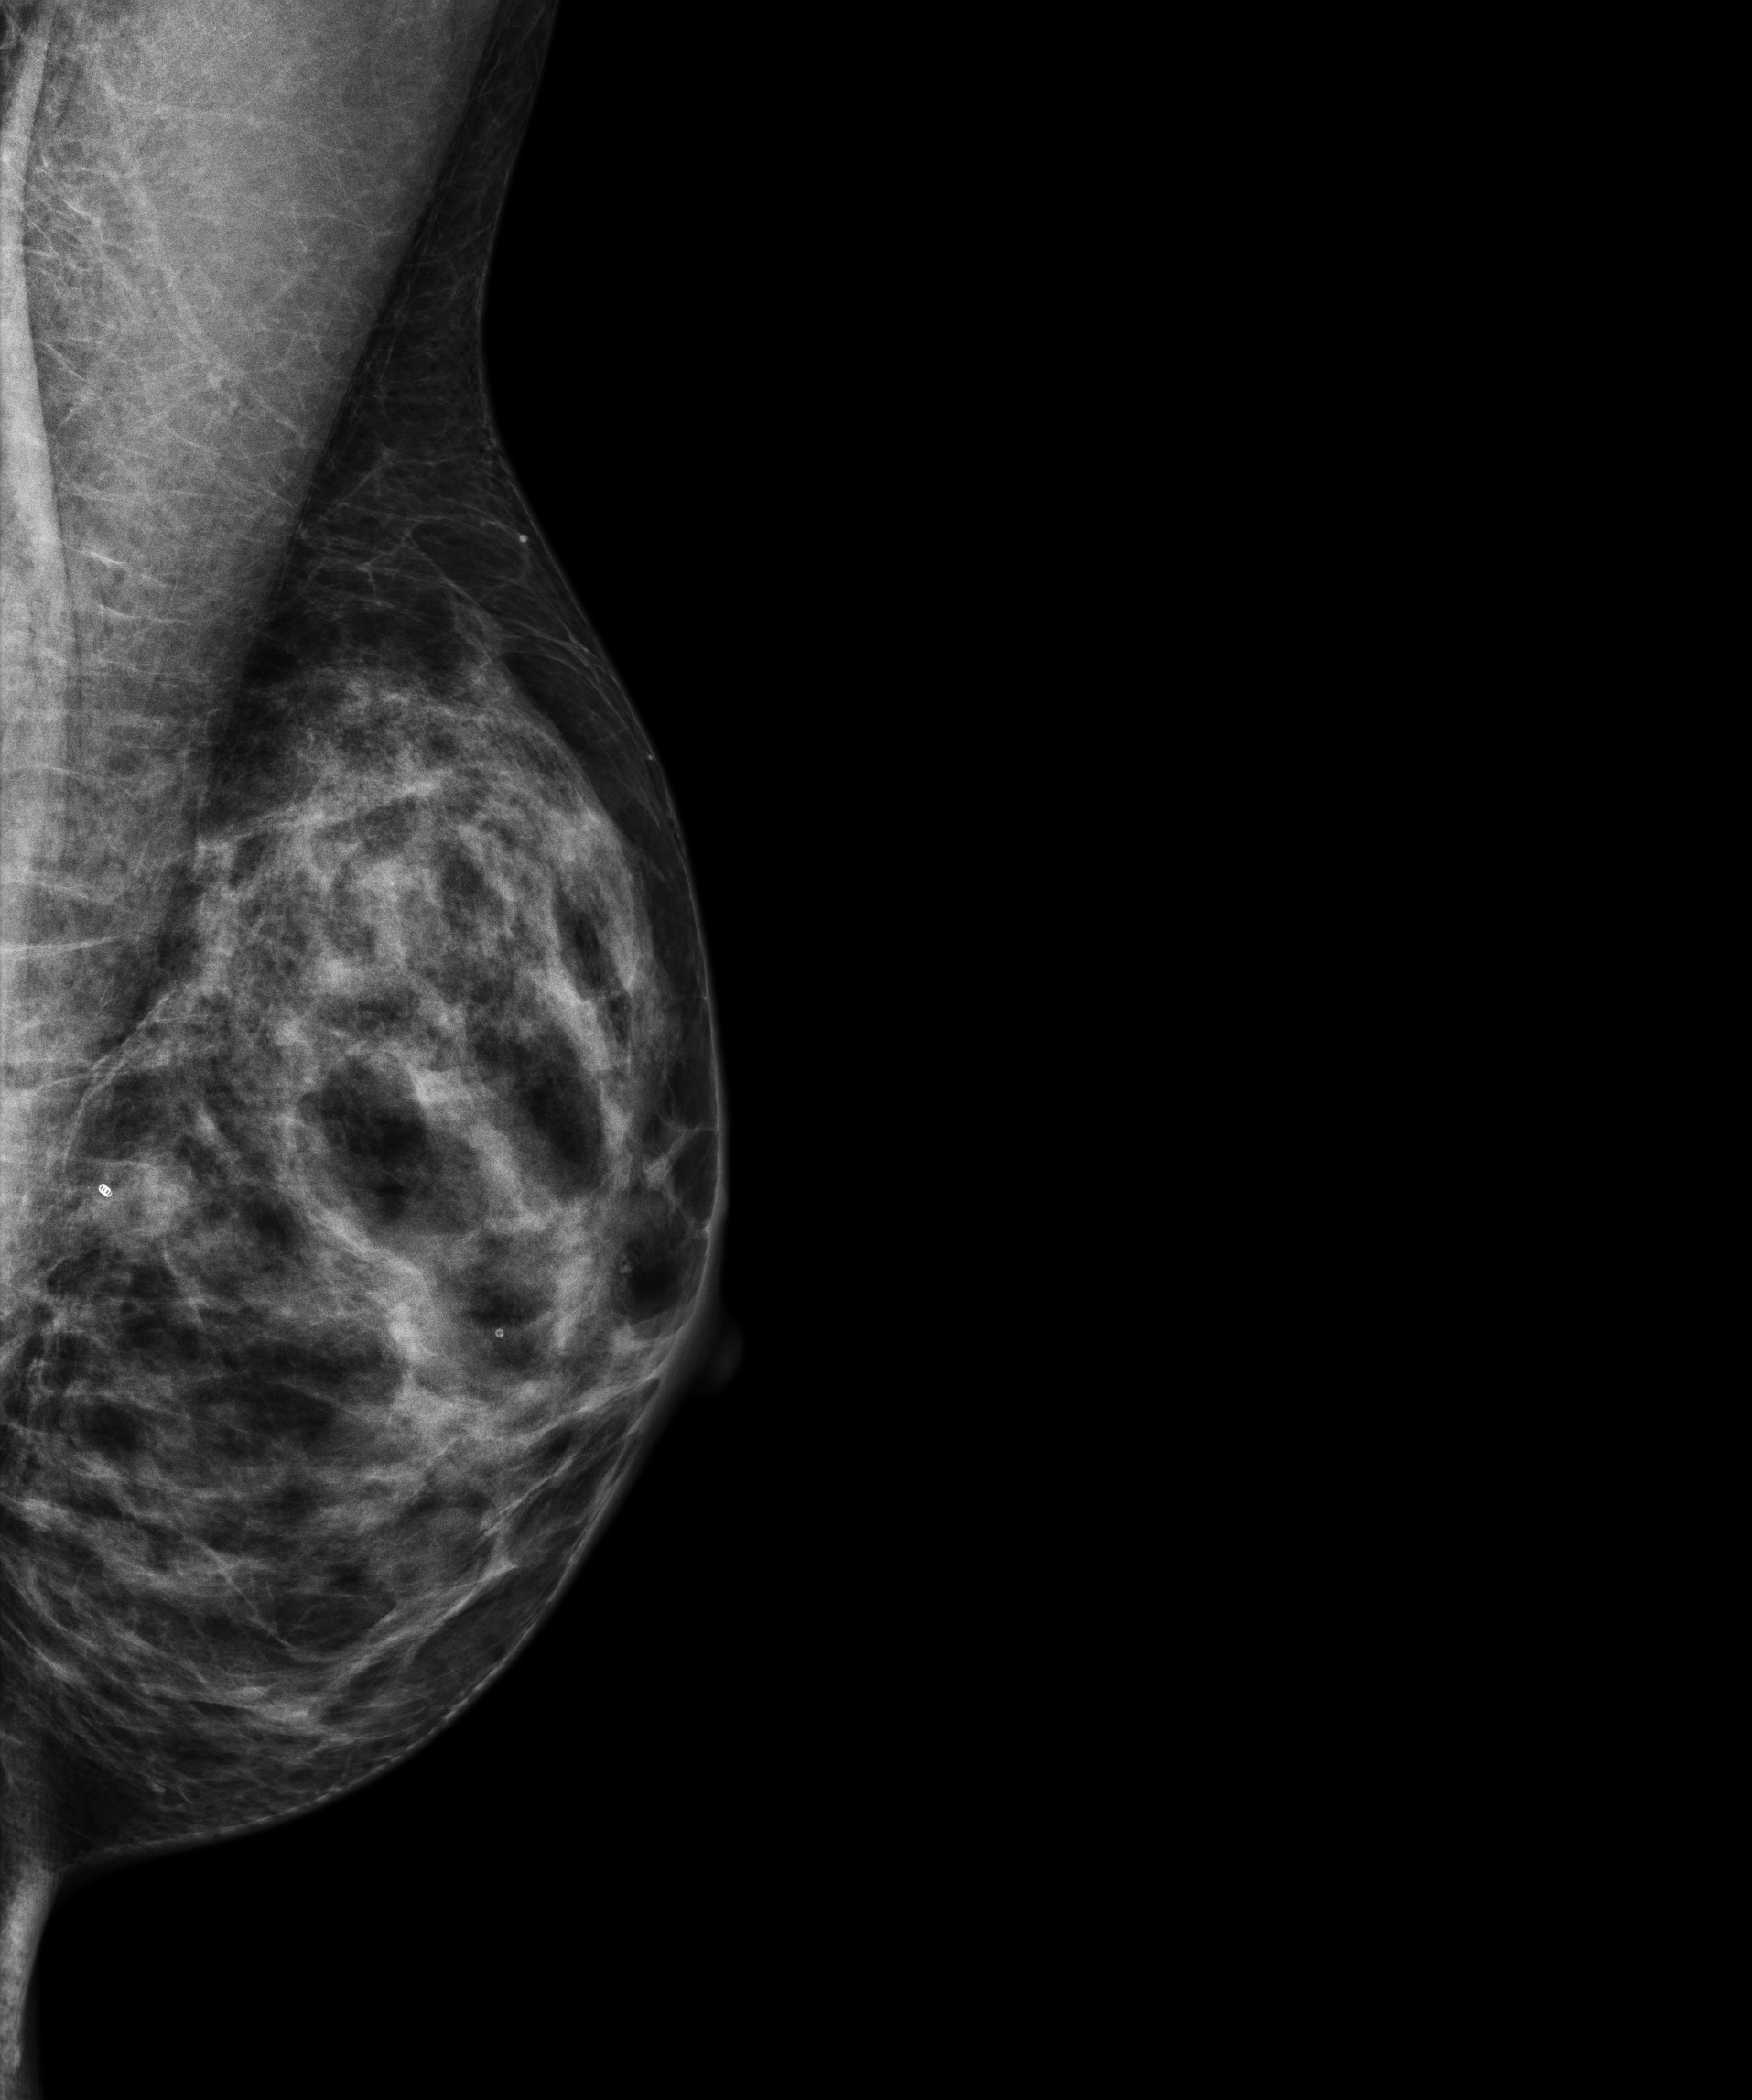
Full-field digital mammogram (FFDM), left breast, MLO view, annual screening mammography examination, compressed breast thickness 47 mm. Female patient, age 43 years.
BI-RADS breast density category at the screening exam (both breasts, scale 1–4): 4. Final BI-RADS assessment for this screening round (tomosynthesis exam, both breasts): category 2. Recall: no recall after this screen.